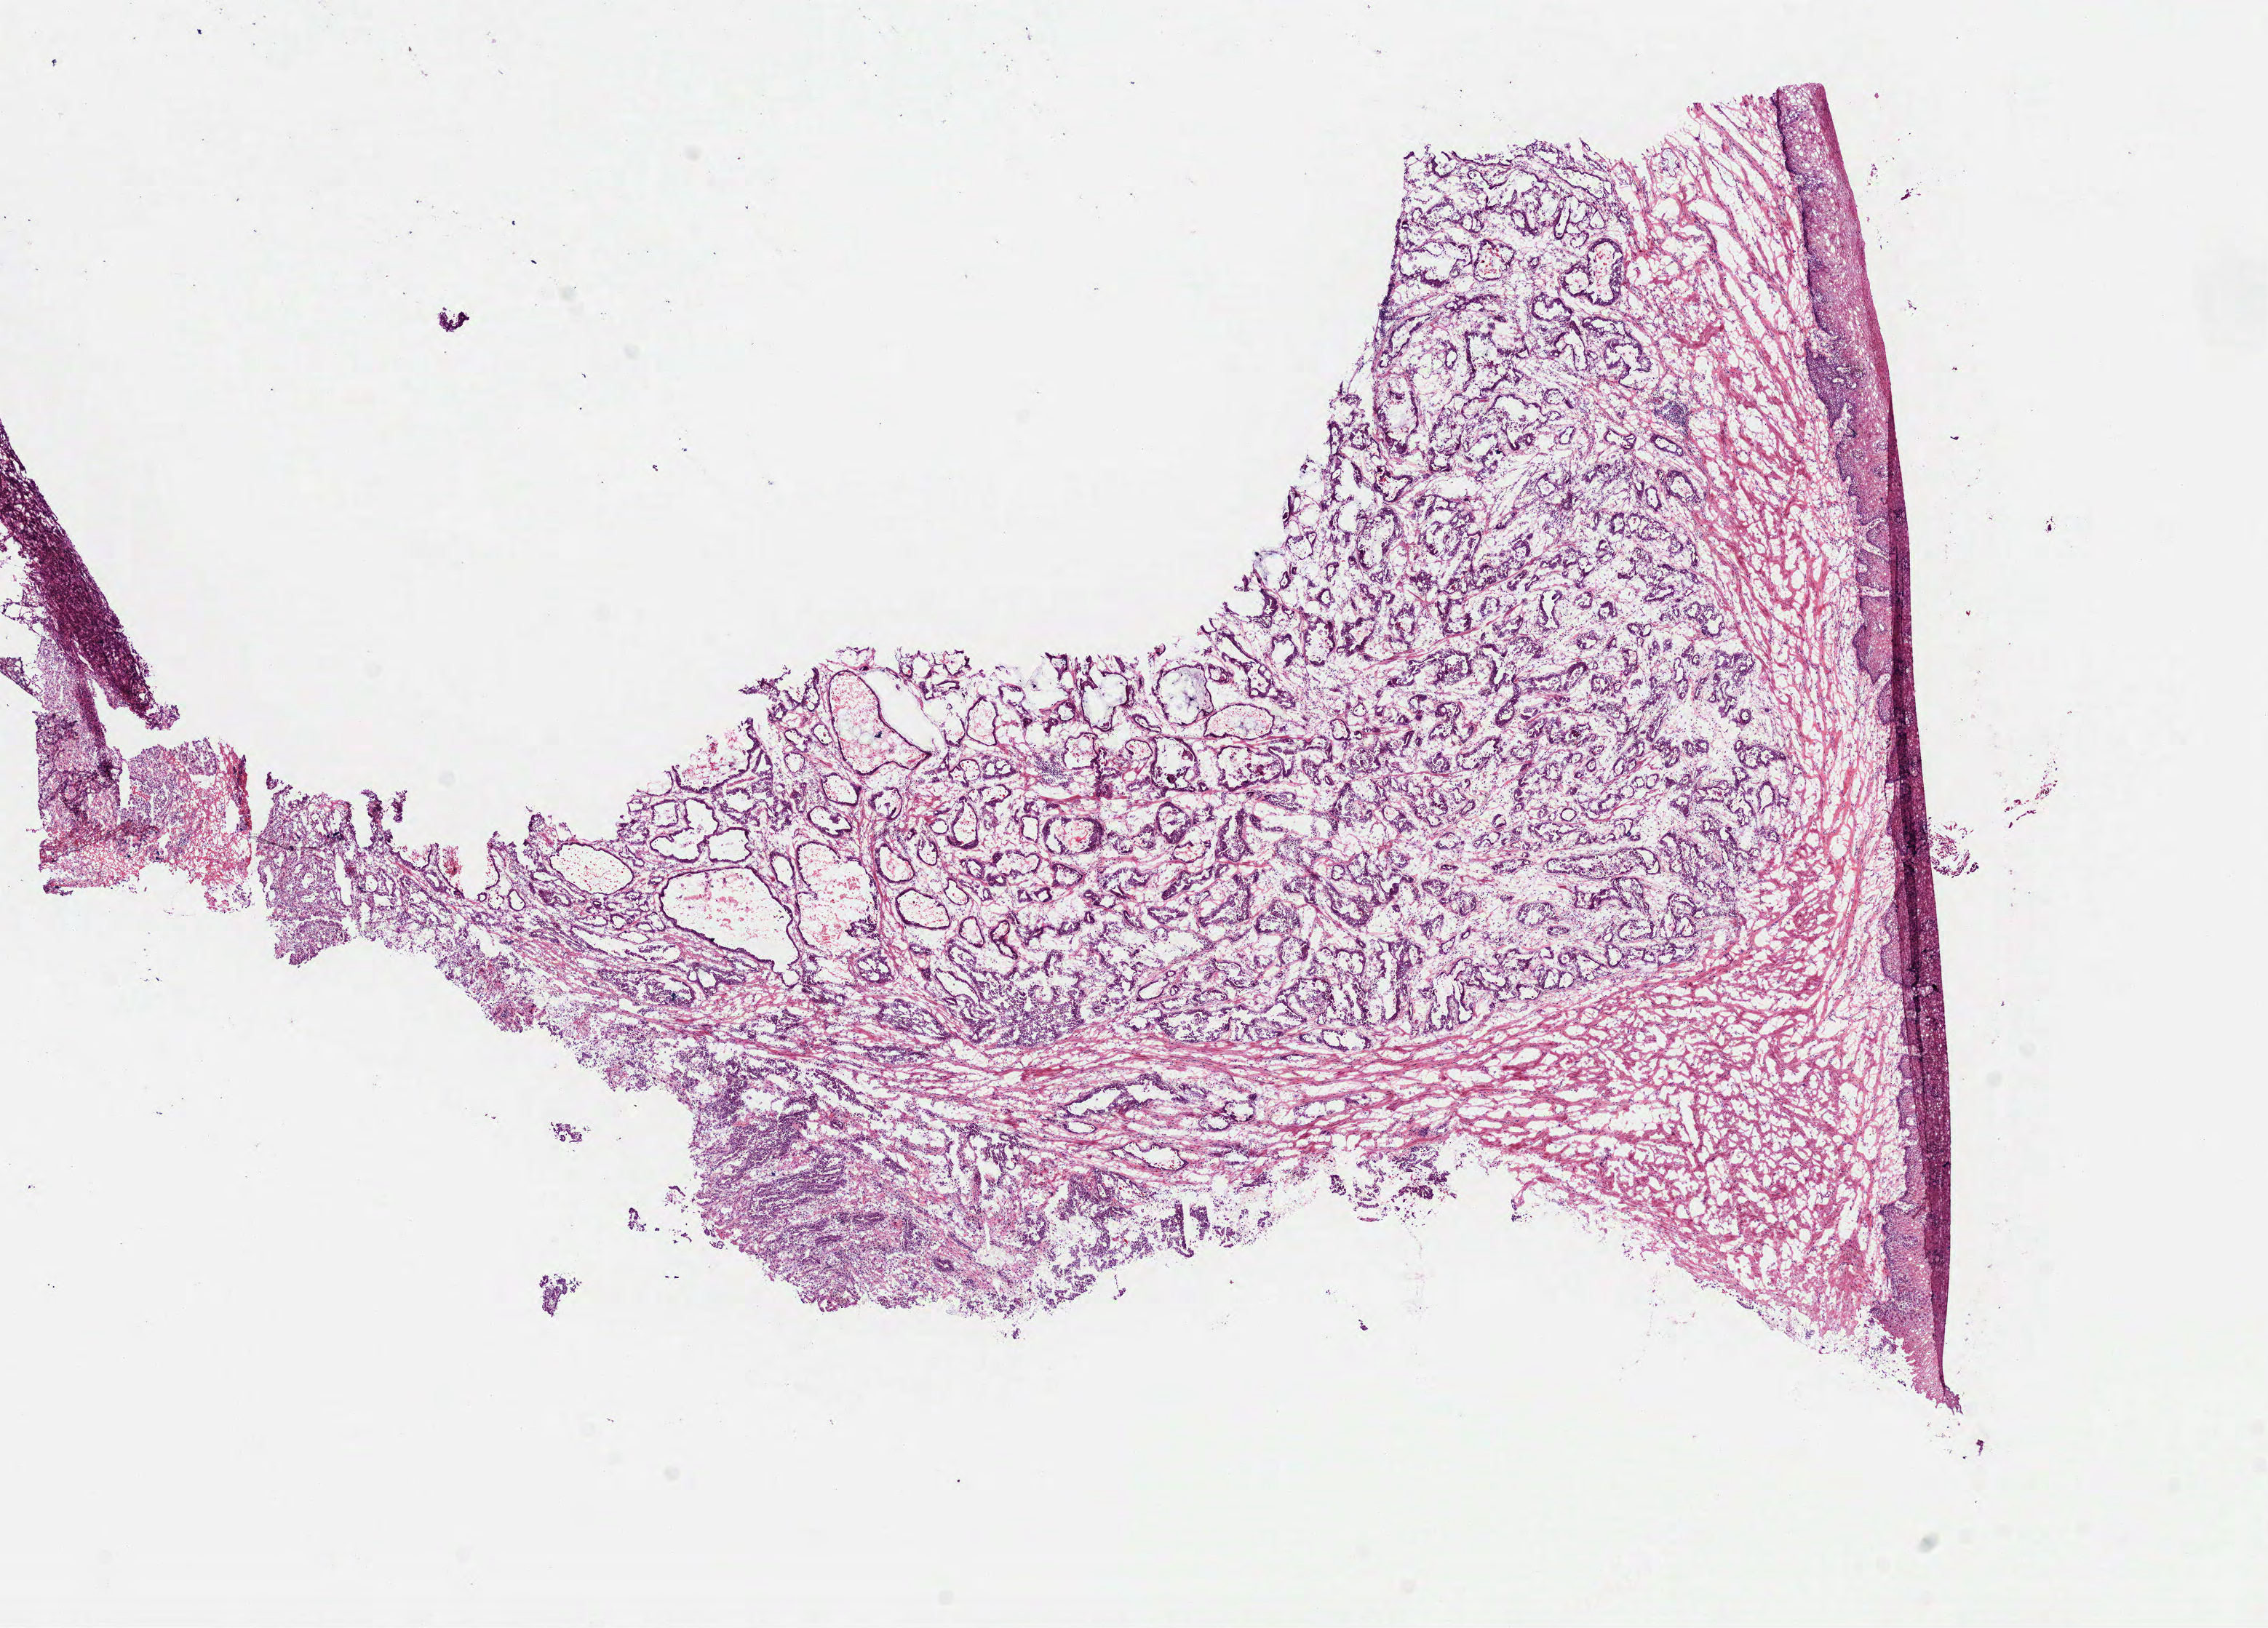
Whole-slide histology image, Hematoxylin and eosin (H&E) stained, low-resolution overview of the scanned area, about 12.6 x 9.0 mm. Frozen section. Stomach, primary tumour sample. Male, age 50 years at initial diagnosis. Histologic grade: G3 (poorly differentiated). Composition of this section per pathologist review: tumour cells 74%, tumour nuclei 70%, normal cells 13%, stromal cells 13%, necrosis 0%. Infiltration values recorded for this section: lymphocyte infiltration 20%, monocyte infiltration 0%, neutrophil infiltration 5%.
AJCC pathologic stage: IIB (7th edition). Histologic diagnosis: Carcinoma, diffuse type (cardia, NOS). Lymph nodes positive (case pathology): 2 of 17 examined.